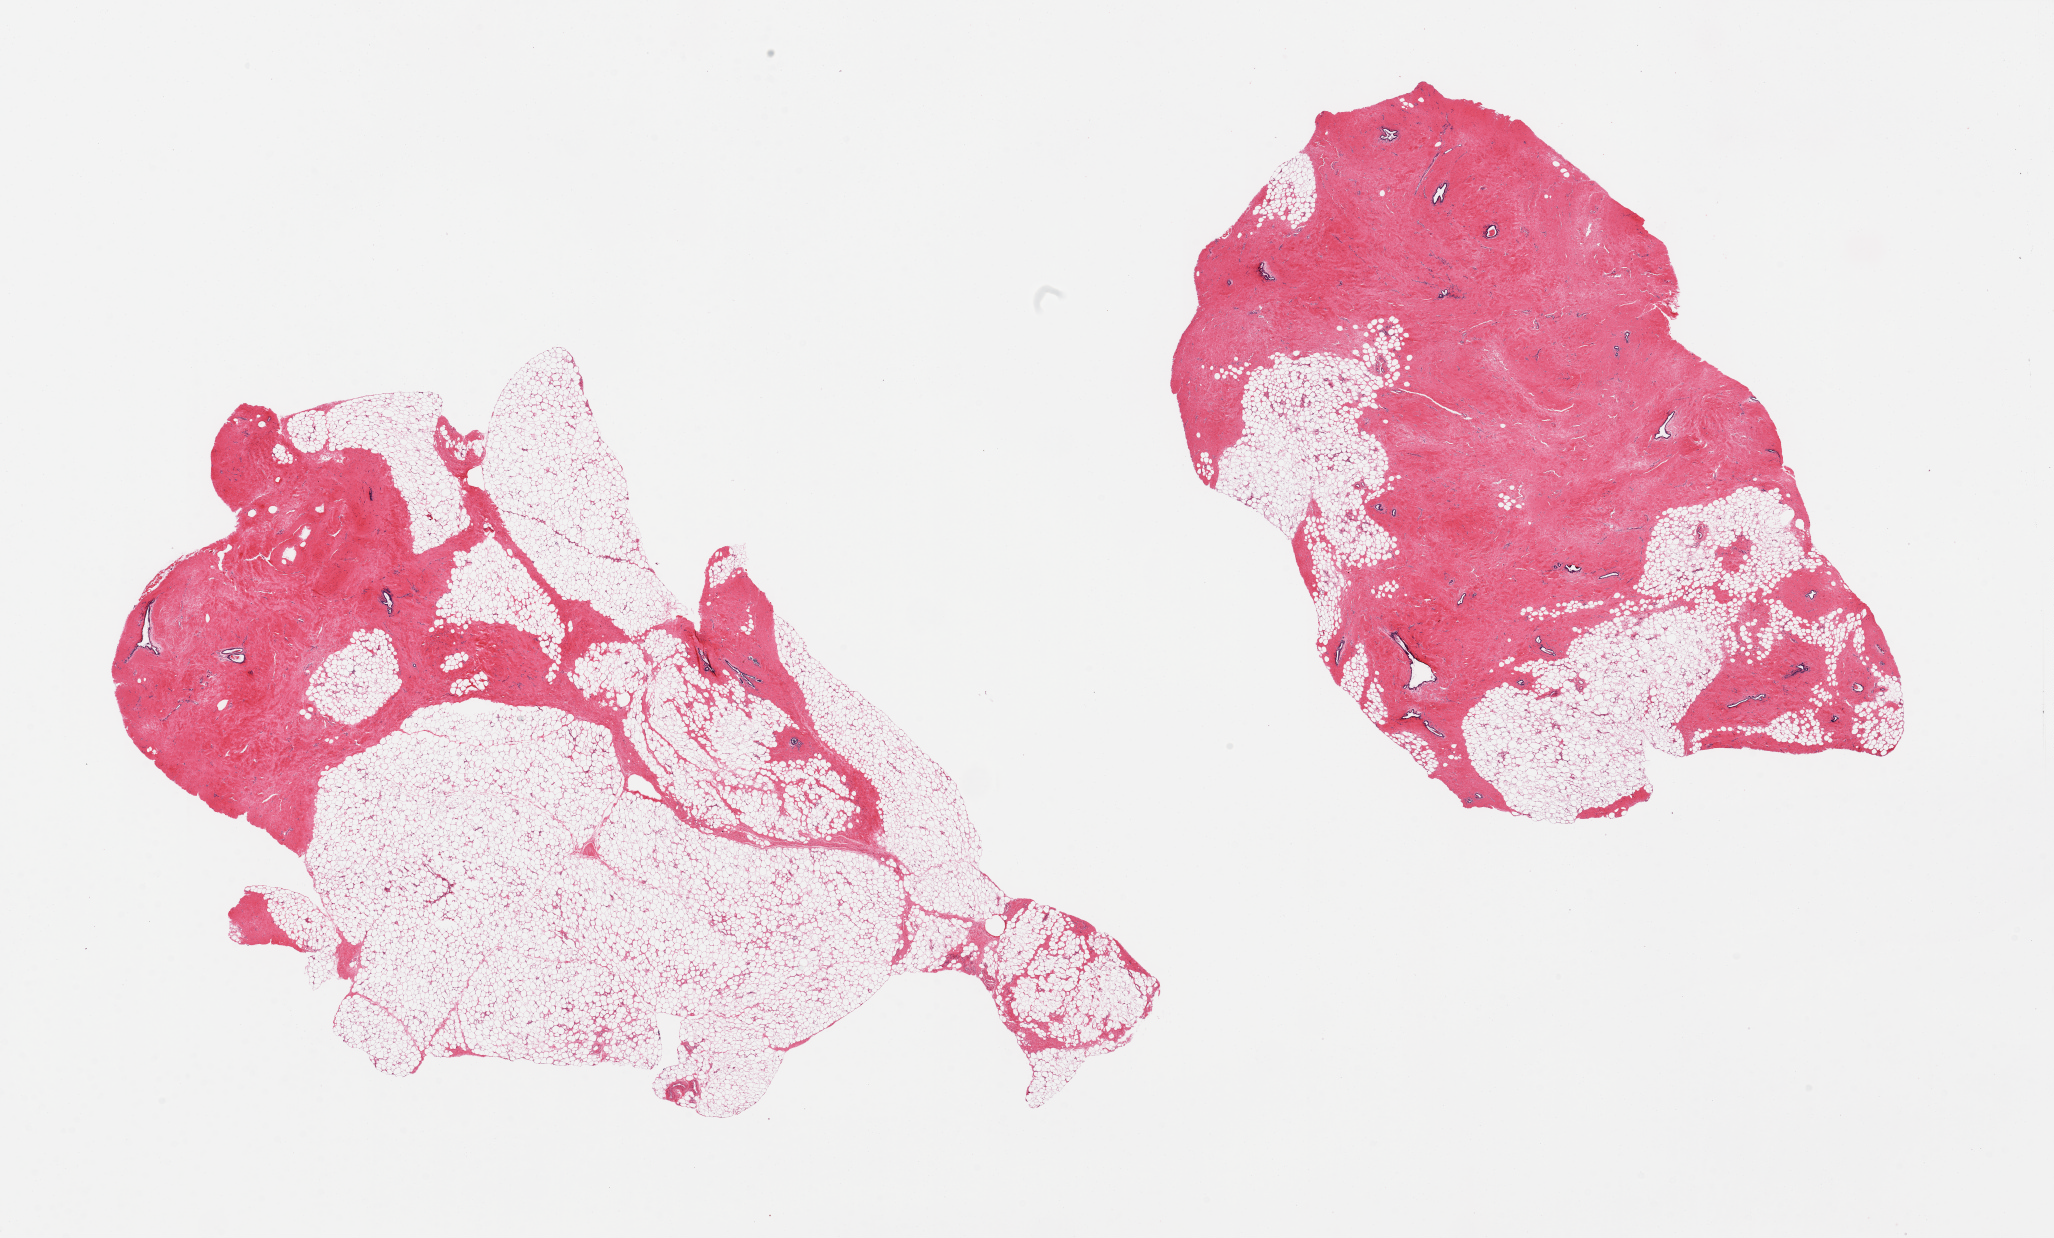
Digitized H&E-stained section, shown as a low-resolution overview of the whole scanned area (about 32.5 x 19.6 mm, from a 20x scan). PAXgene-fixed paraffin-embedded (PFPE) section. Section of breast (target tissue). Donor tissue sample. Donor: male.
* reviewer comment on this tissue sample: 2 pieces, gynecomatoid stromal hyperplasia, ductal elements present